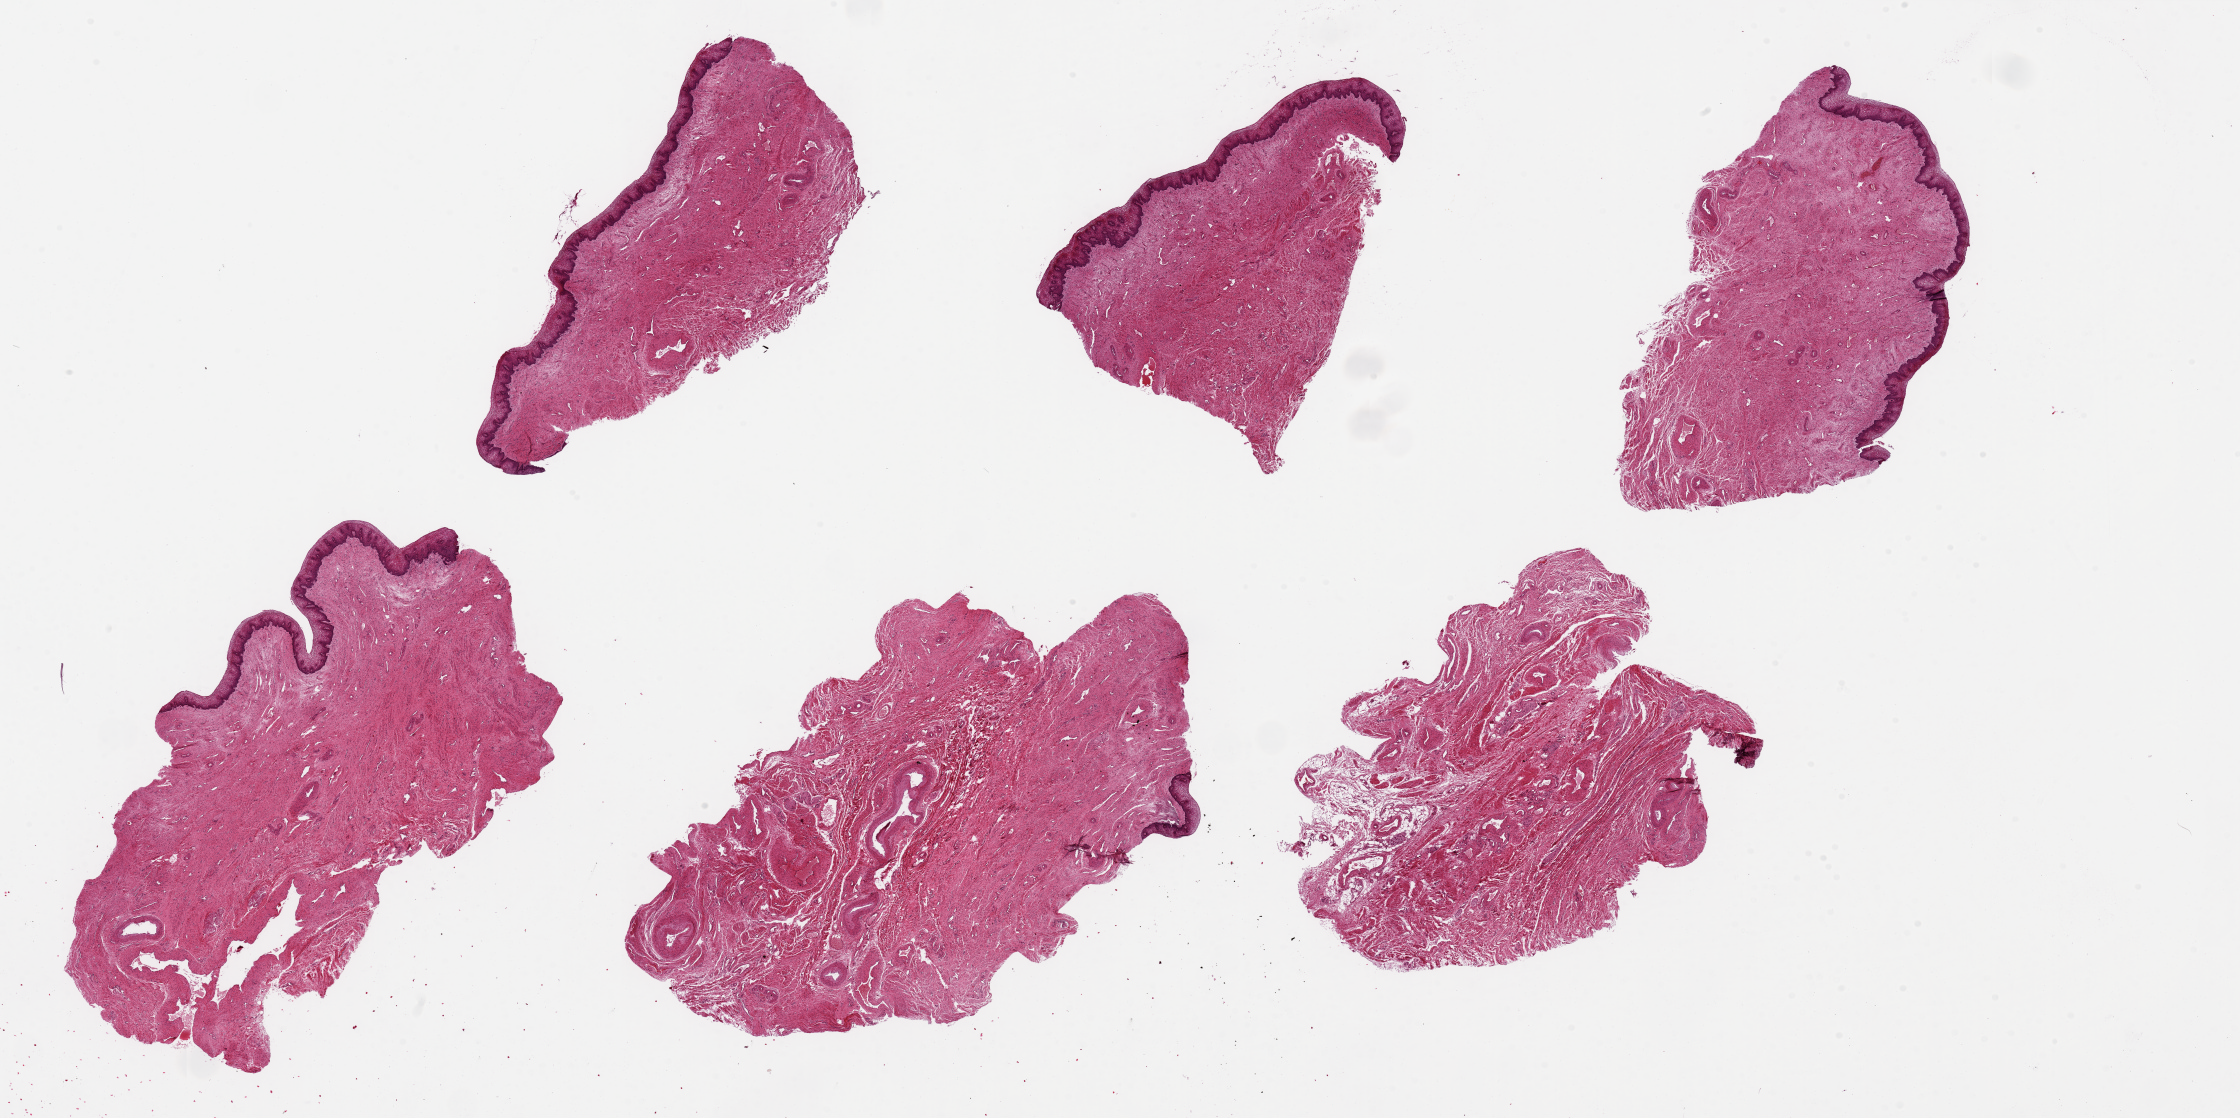
Whole-slide image, haematoxylin and eosin stain — shown as a low-resolution overview of the whole scanned area (about 35.4 x 17.7 mm, slide scanned at 20x), PAXgene-fixed paraffin-embedded (PFPE) section, section of vagina (target tissue), donor tissue sample. Female donor.
* review note (as recorded): 6 pieces ~7x3mm, squmaous mucosa reasonably well preserved, ~5-10% of thickness